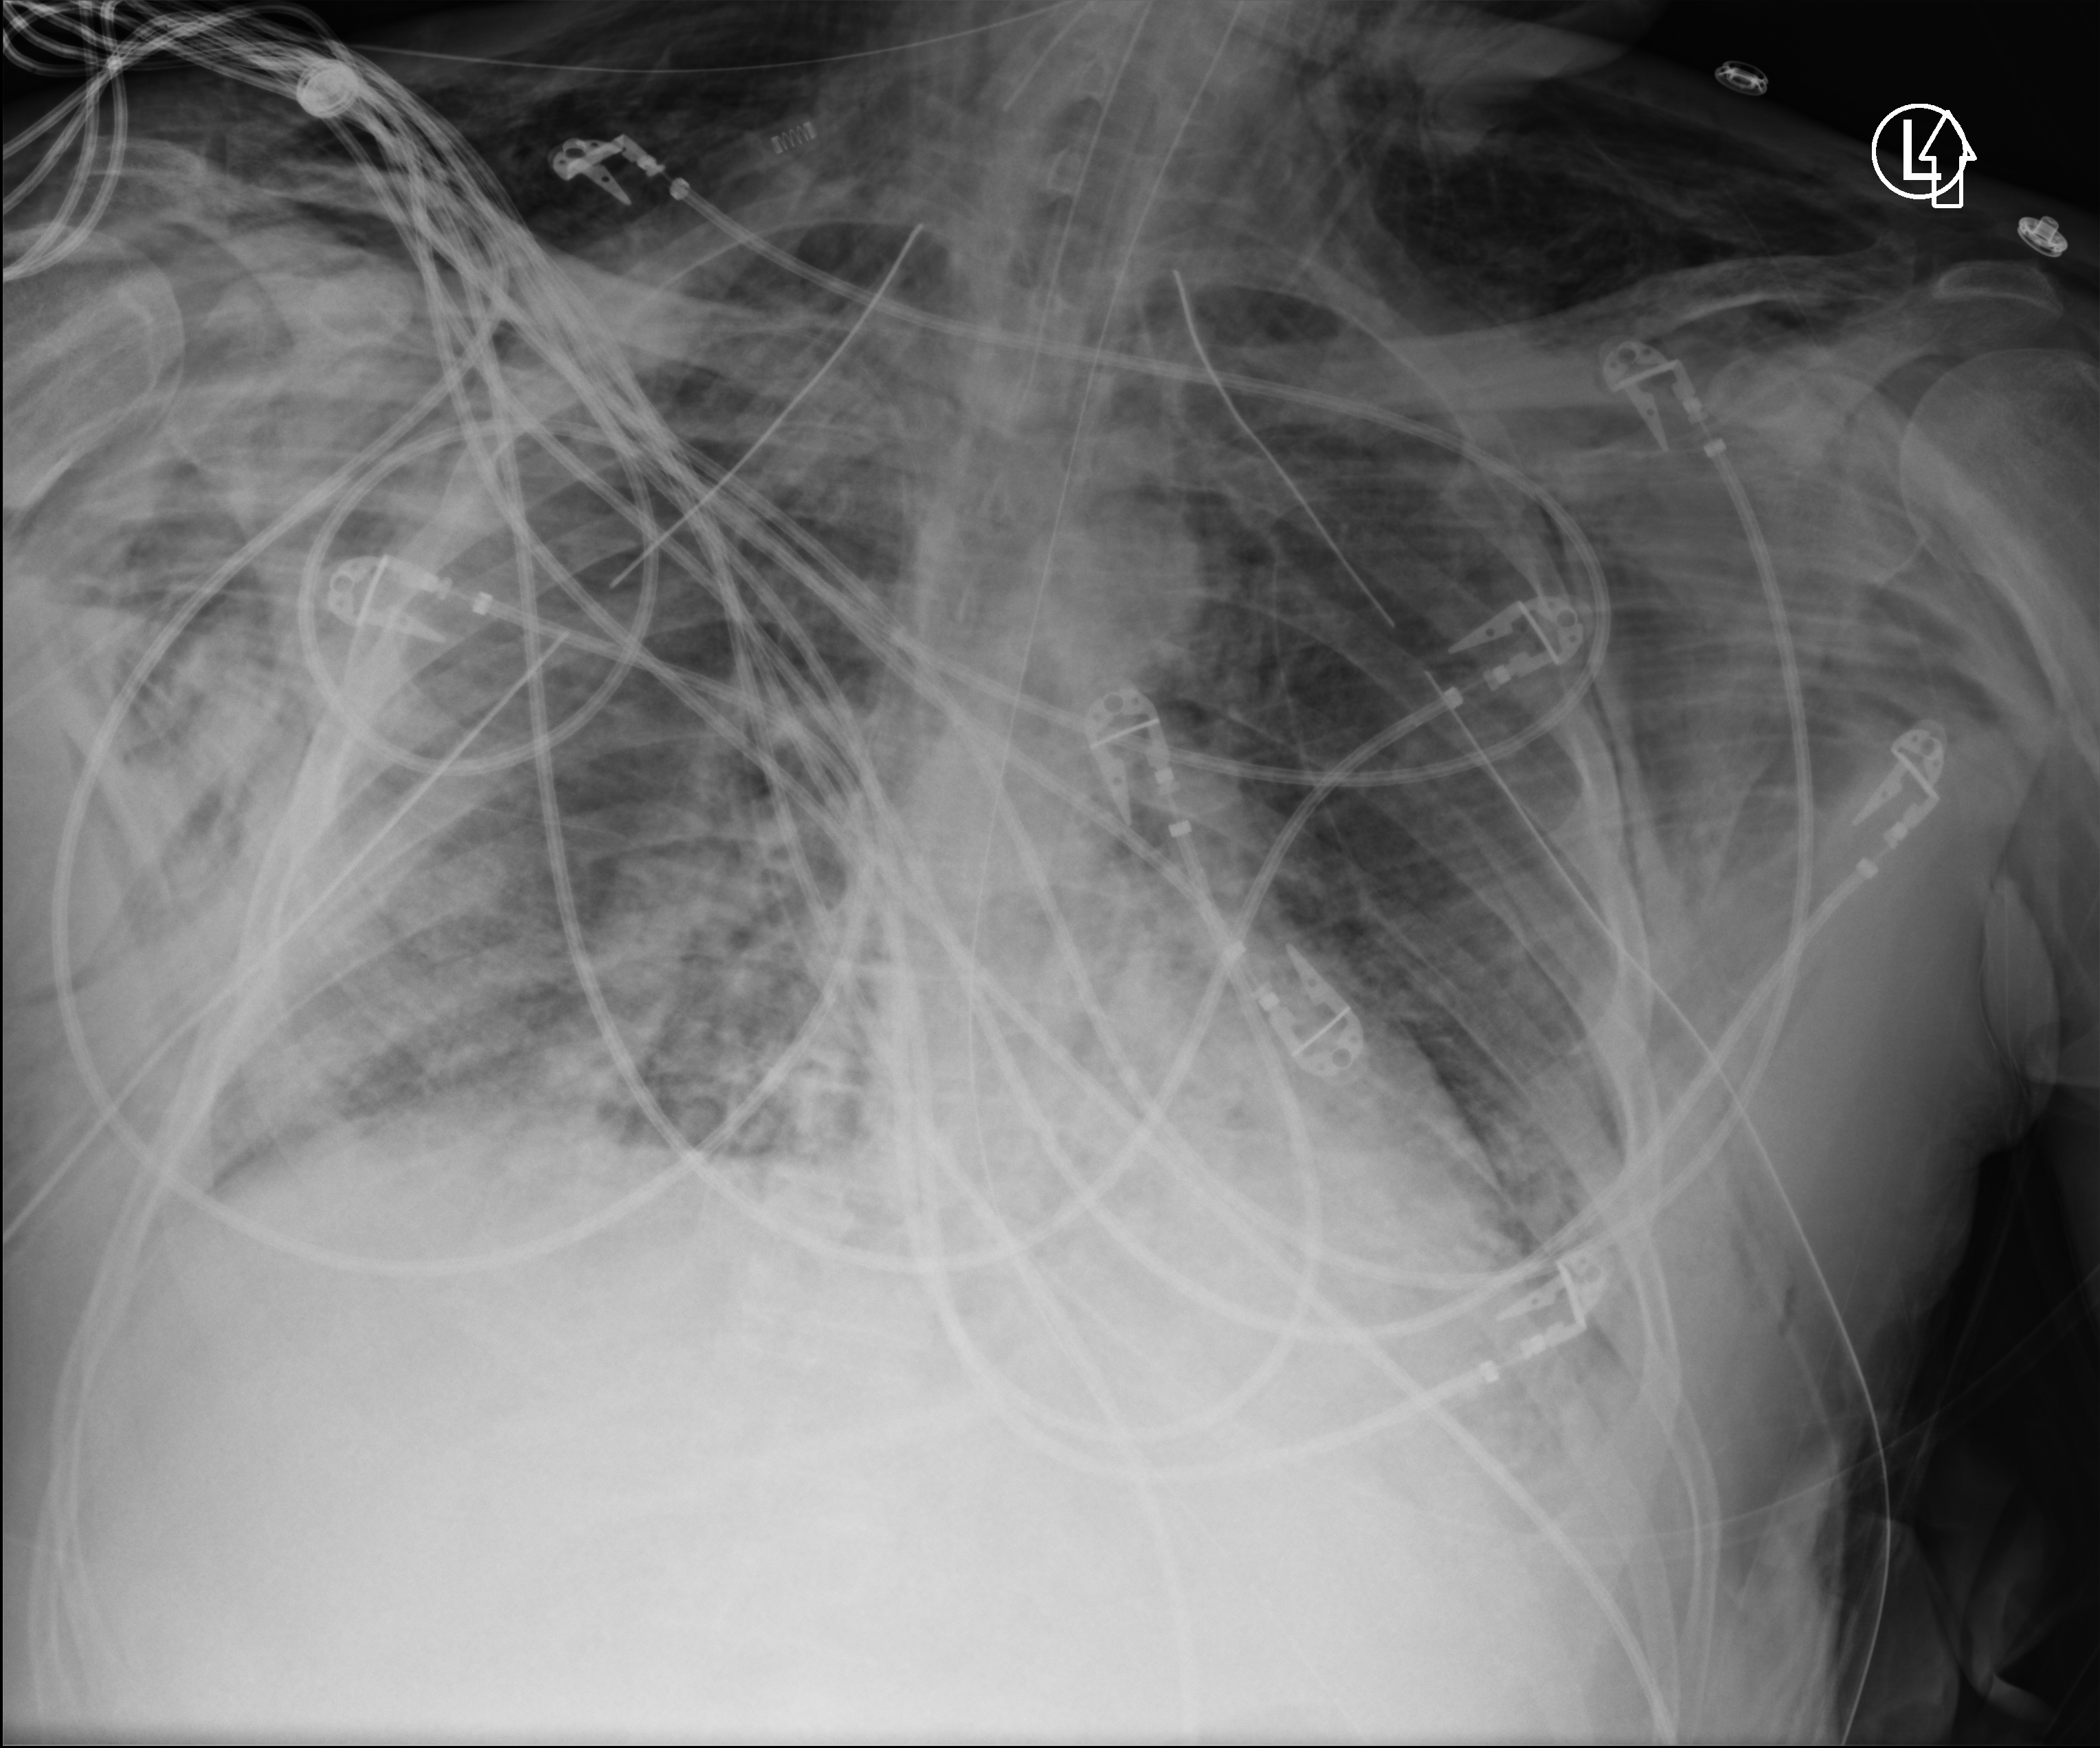
Chest X-ray (portable); anteroposterior (AP) projection. Patient hospitalised with COVID-19; male, aged 18–59 years.
Admission-level facts for this patient (not findings on this image; timing relative to this image not recorded): admitted to intensive care during this hospital stay: yes.